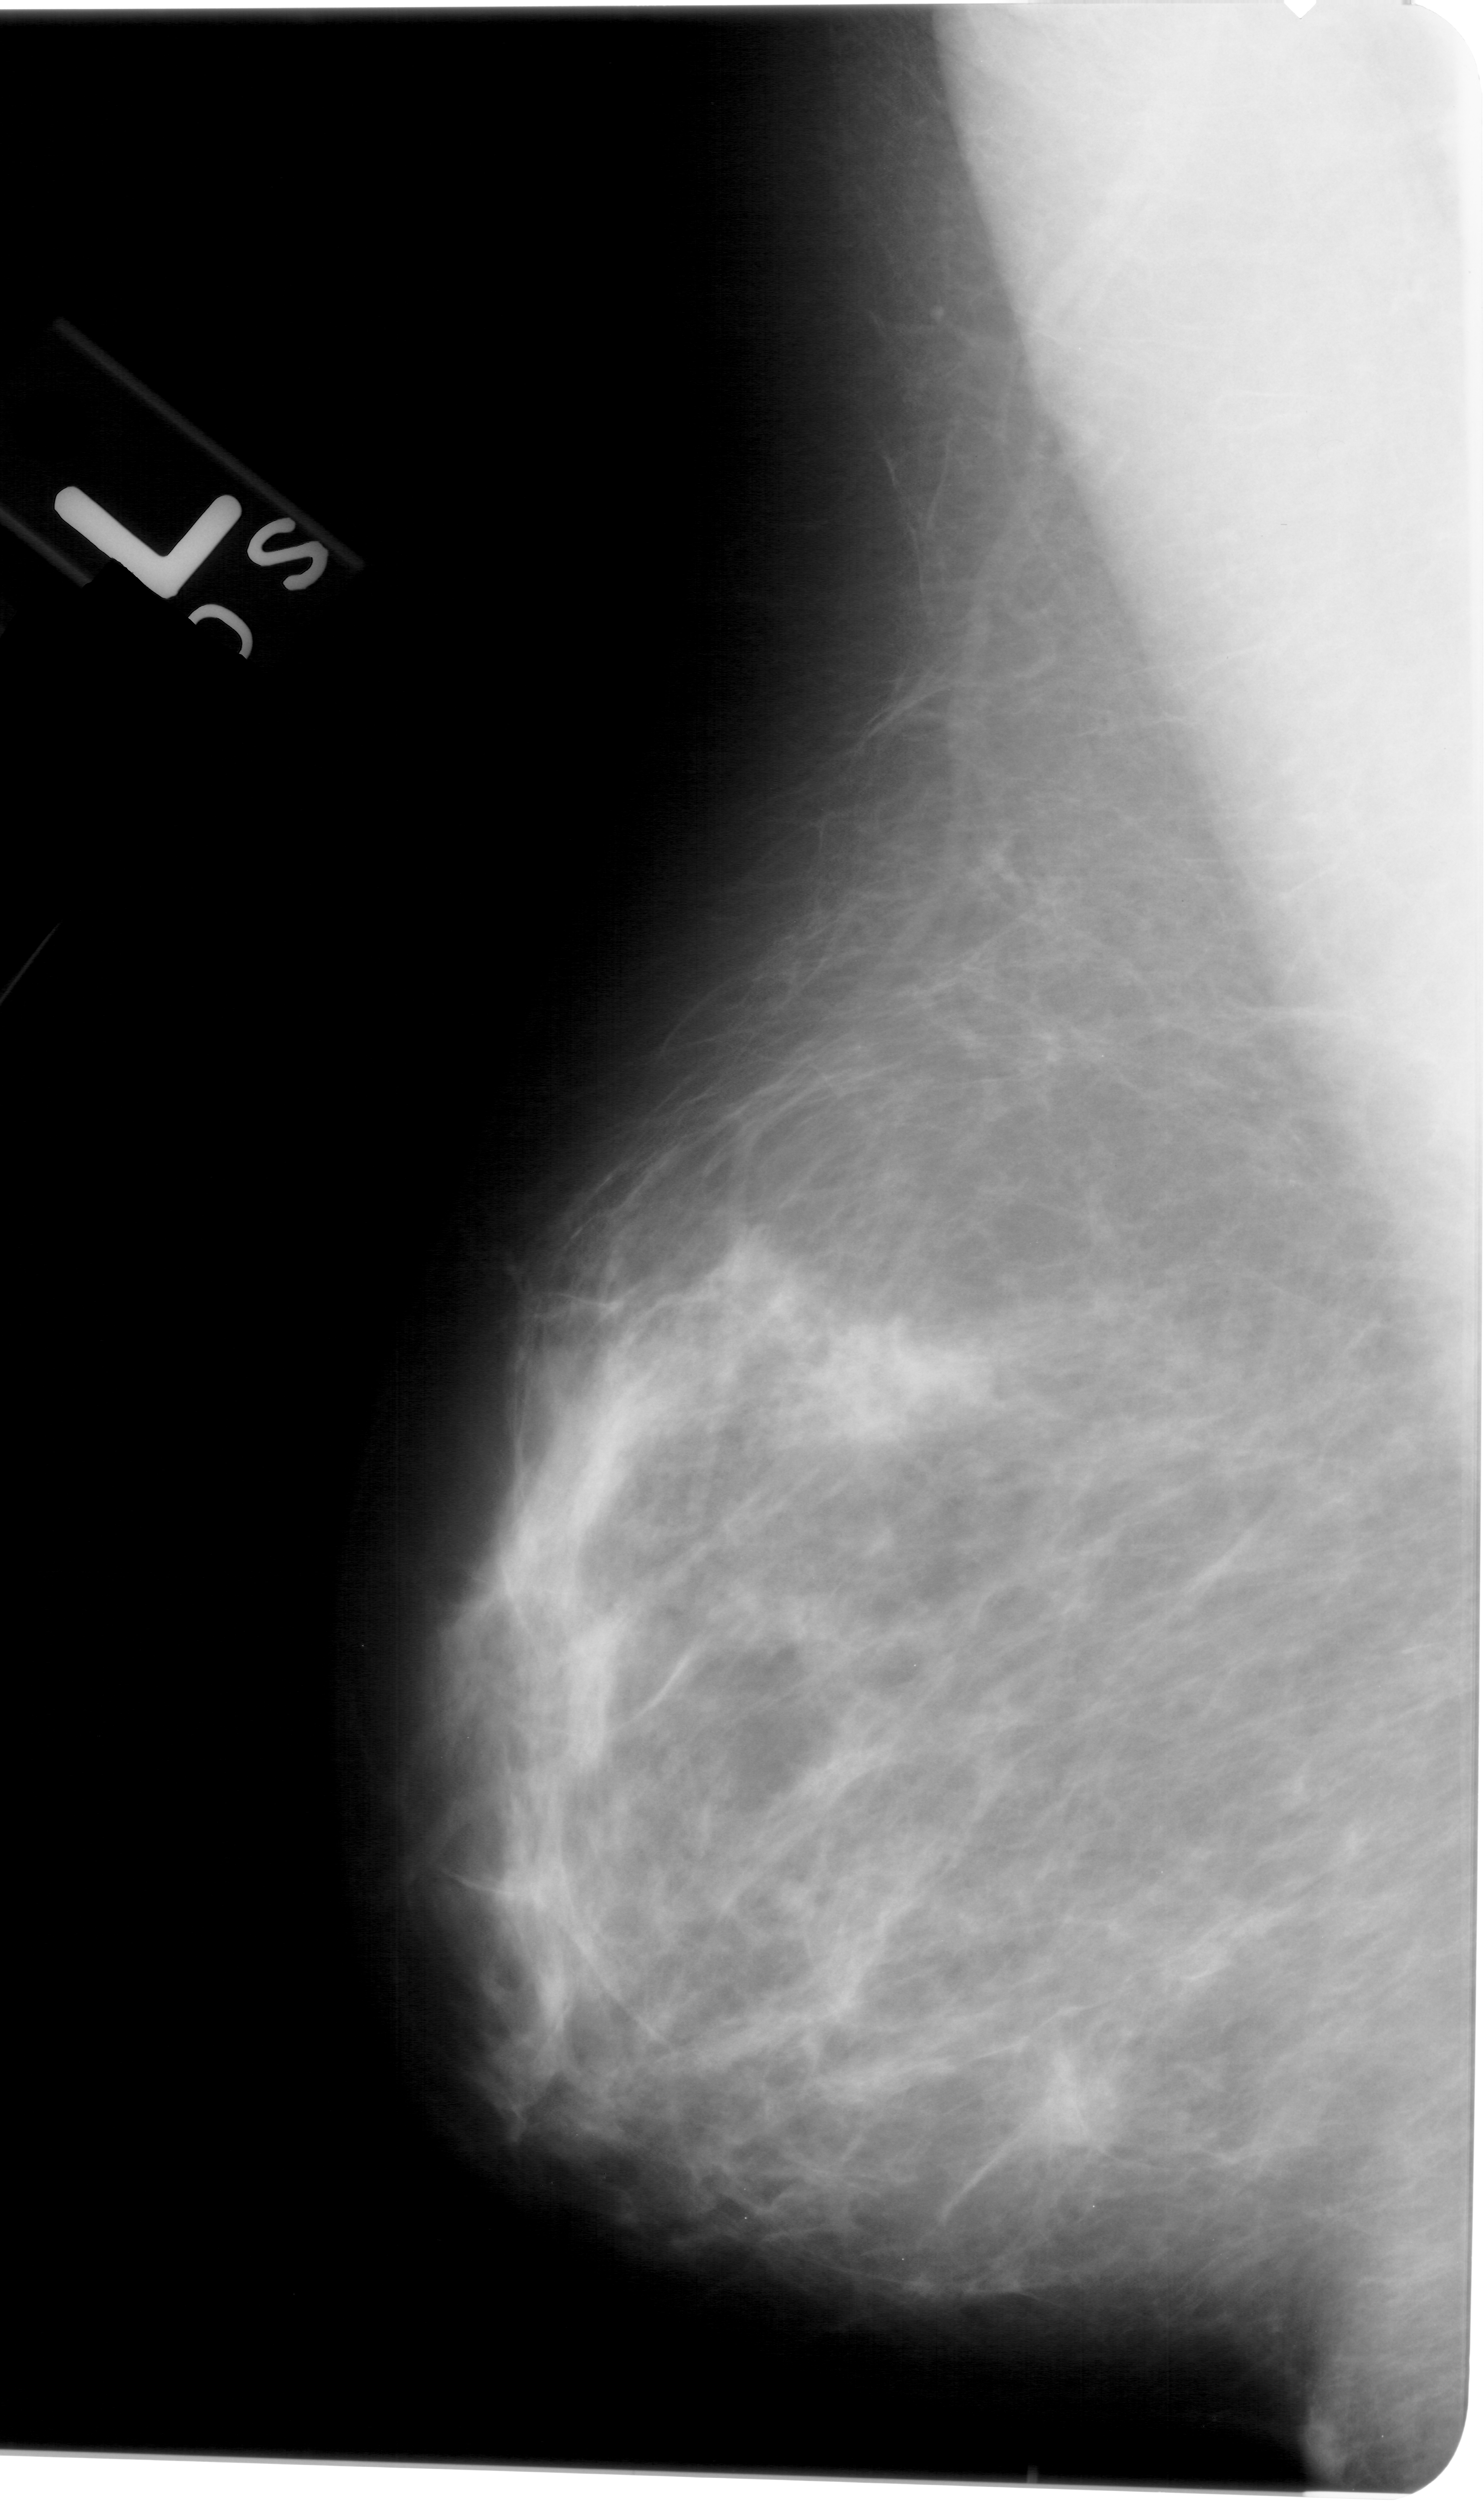
Digitized screen-film mammogram, left breast, mediolateral oblique (MLO) view, BI-RADS breast density category 3 (scale 1–4).
- Marked findings (only marked abnormalities are described; nothing is implied about the rest of the image): mass, shape oval, margins obscured / ill defined; BI-RADS assessment category 4; pathology (as recorded): benign.